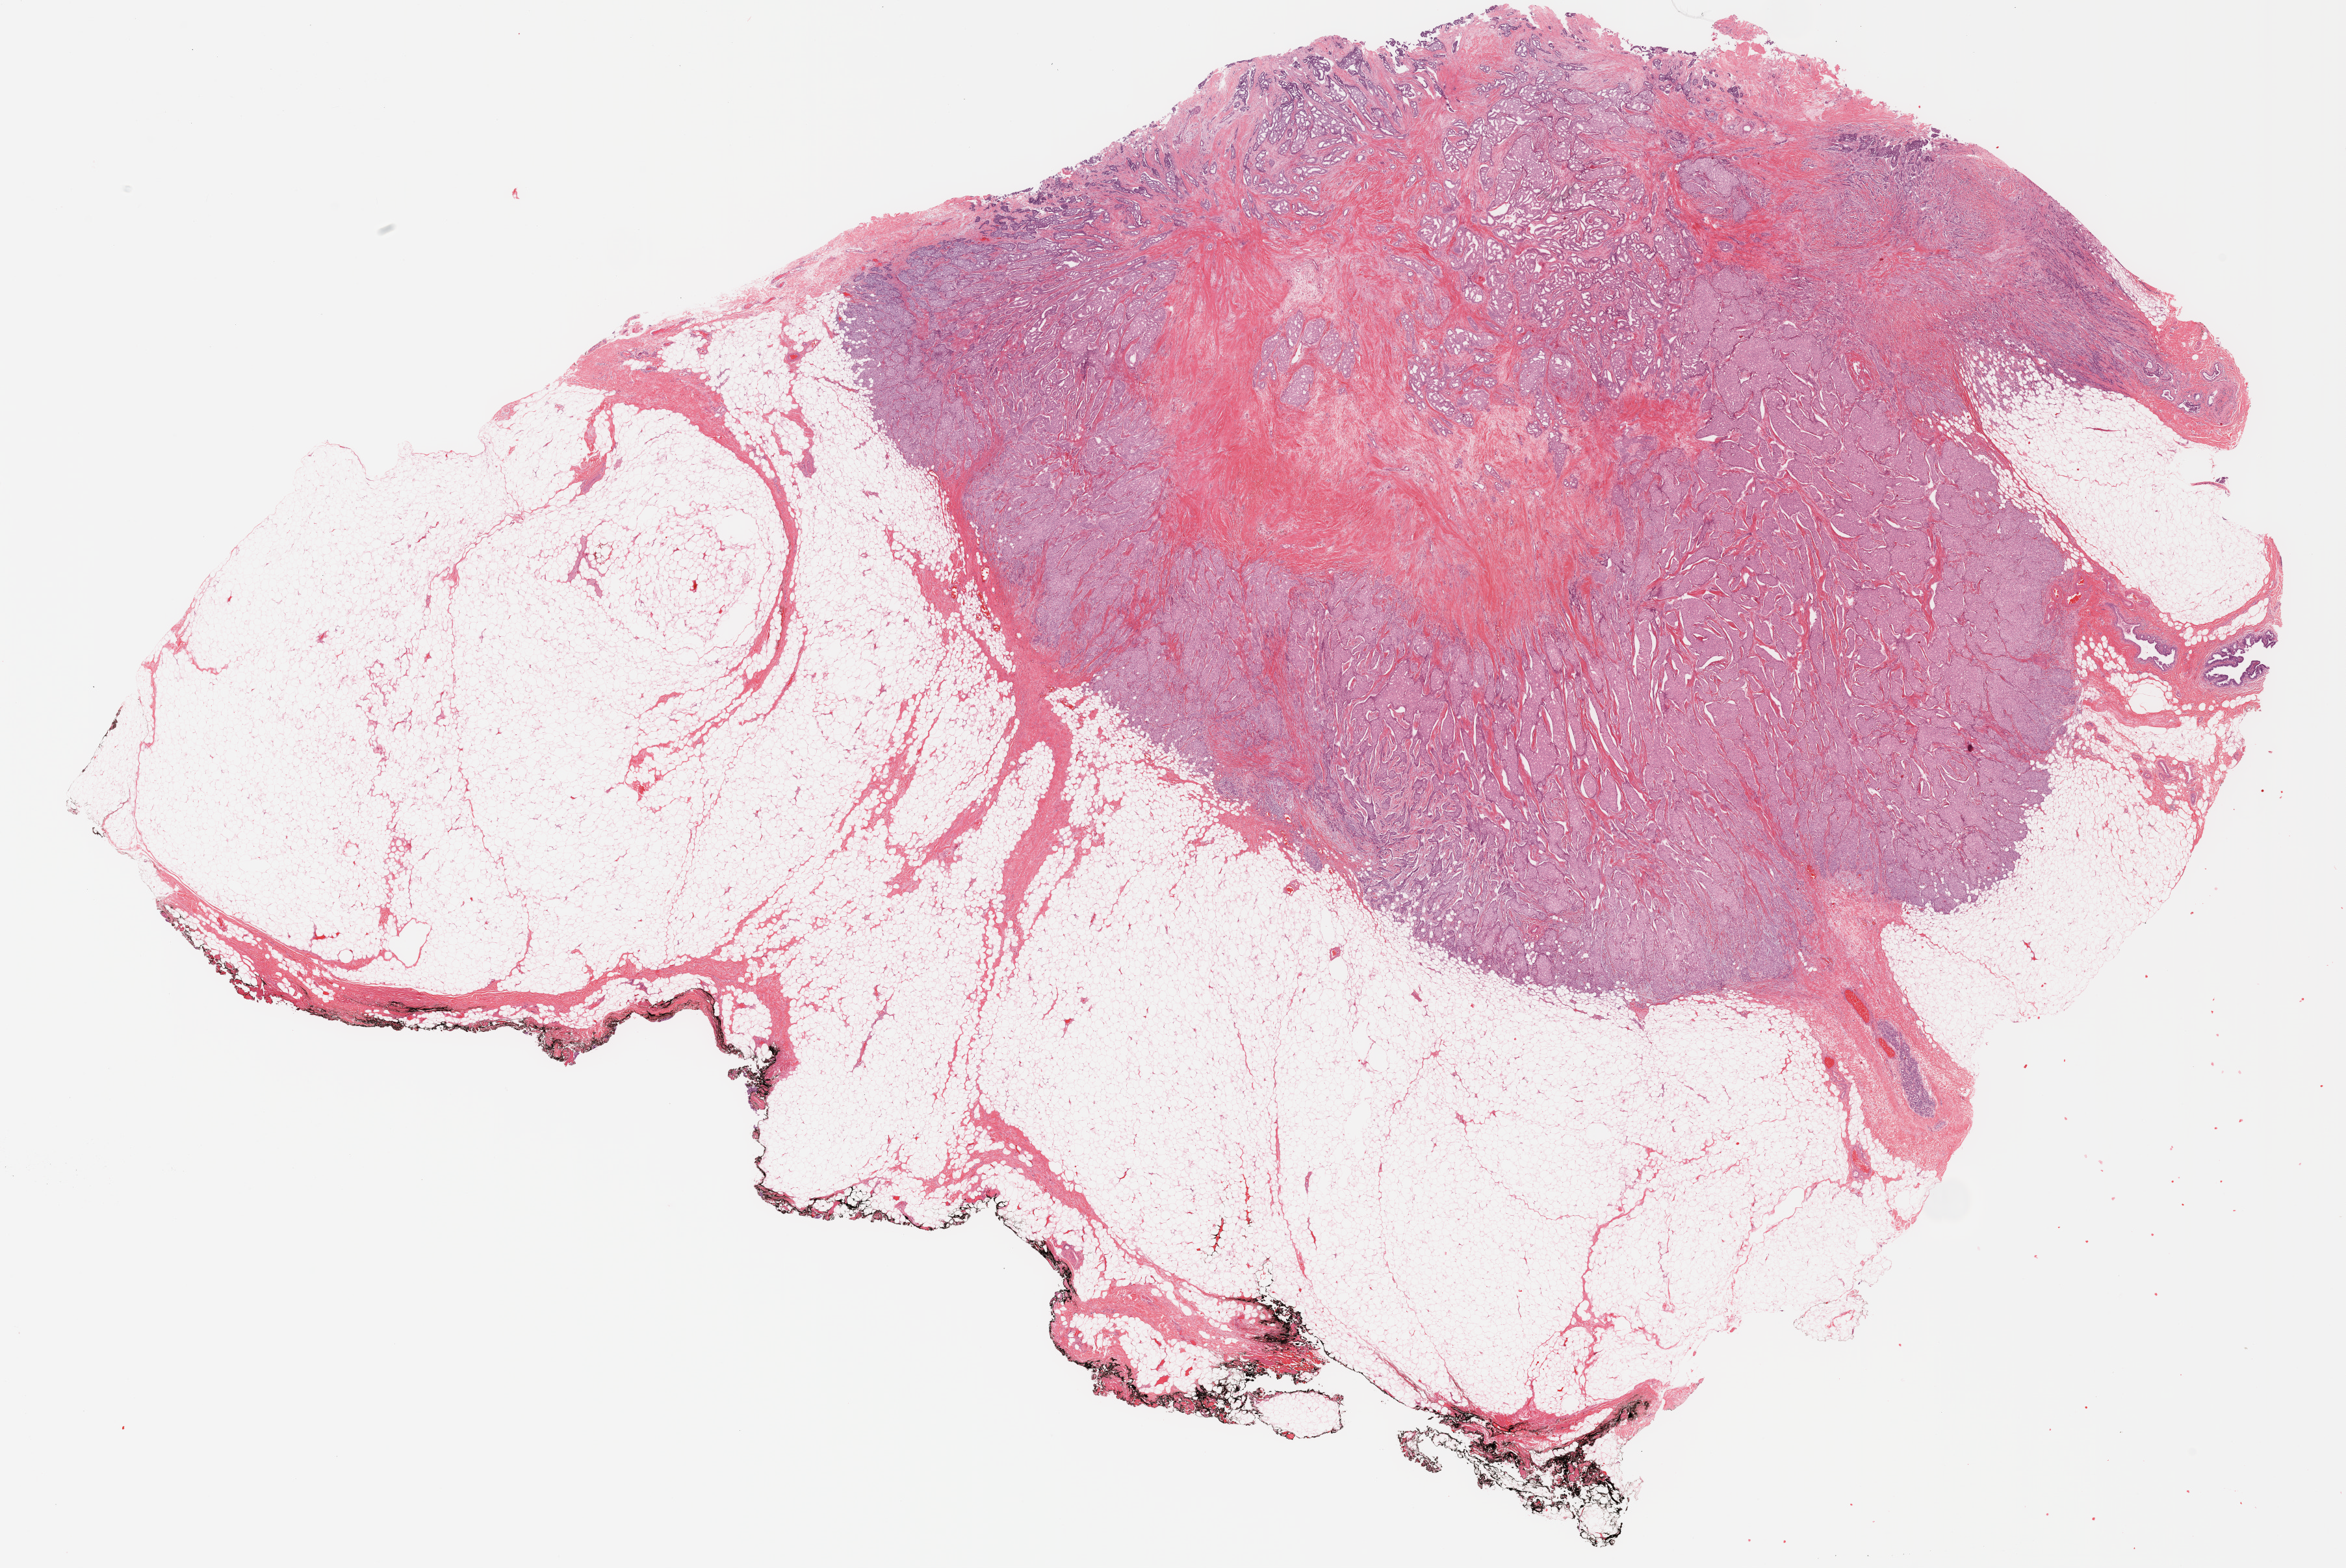
Whole-slide histology image, H&E-stained — a low-resolution overview of the entire scanned area, about 28.8 x 19.3 mm; formalin-fixed paraffin-embedded (FFPE) diagnostic section; primary tumour sample from the breast. Female patient; age at initial diagnosis 39 years.
Histologic diagnosis: Infiltrating duct carcinoma, NOS. Lymph nodes positive (case pathology): 0 of 5 examined. Laterality: right. AJCC pathologic stage: IIA.